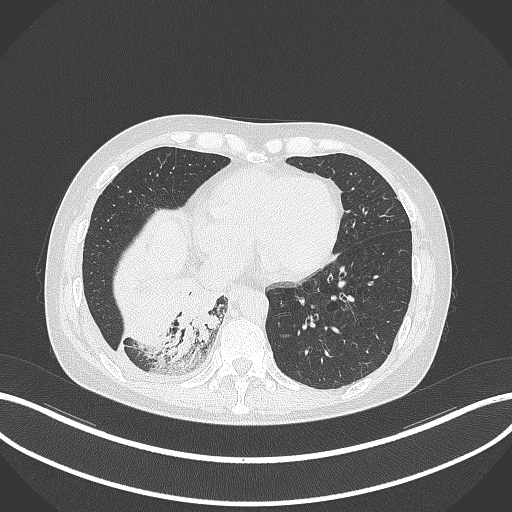
Chest CT, one axial slice; slice 91 of 329 in the series (ordered by position); reconstruction kernel B70f; lung window (W 1500 / L -600 HU); 512 × 512 image matrix. Patient: female, 63 years. From the clinical record (not read from this slice): clinical TNM (as recorded): T1c N0 M0.
Outlined on this slice (bounding box drawn by a radiologist):
- lung tumour (recorded histology: adenocarcinoma): bounding box (x1, y1, x2, y2) in pixels: (172, 283, 230, 359)